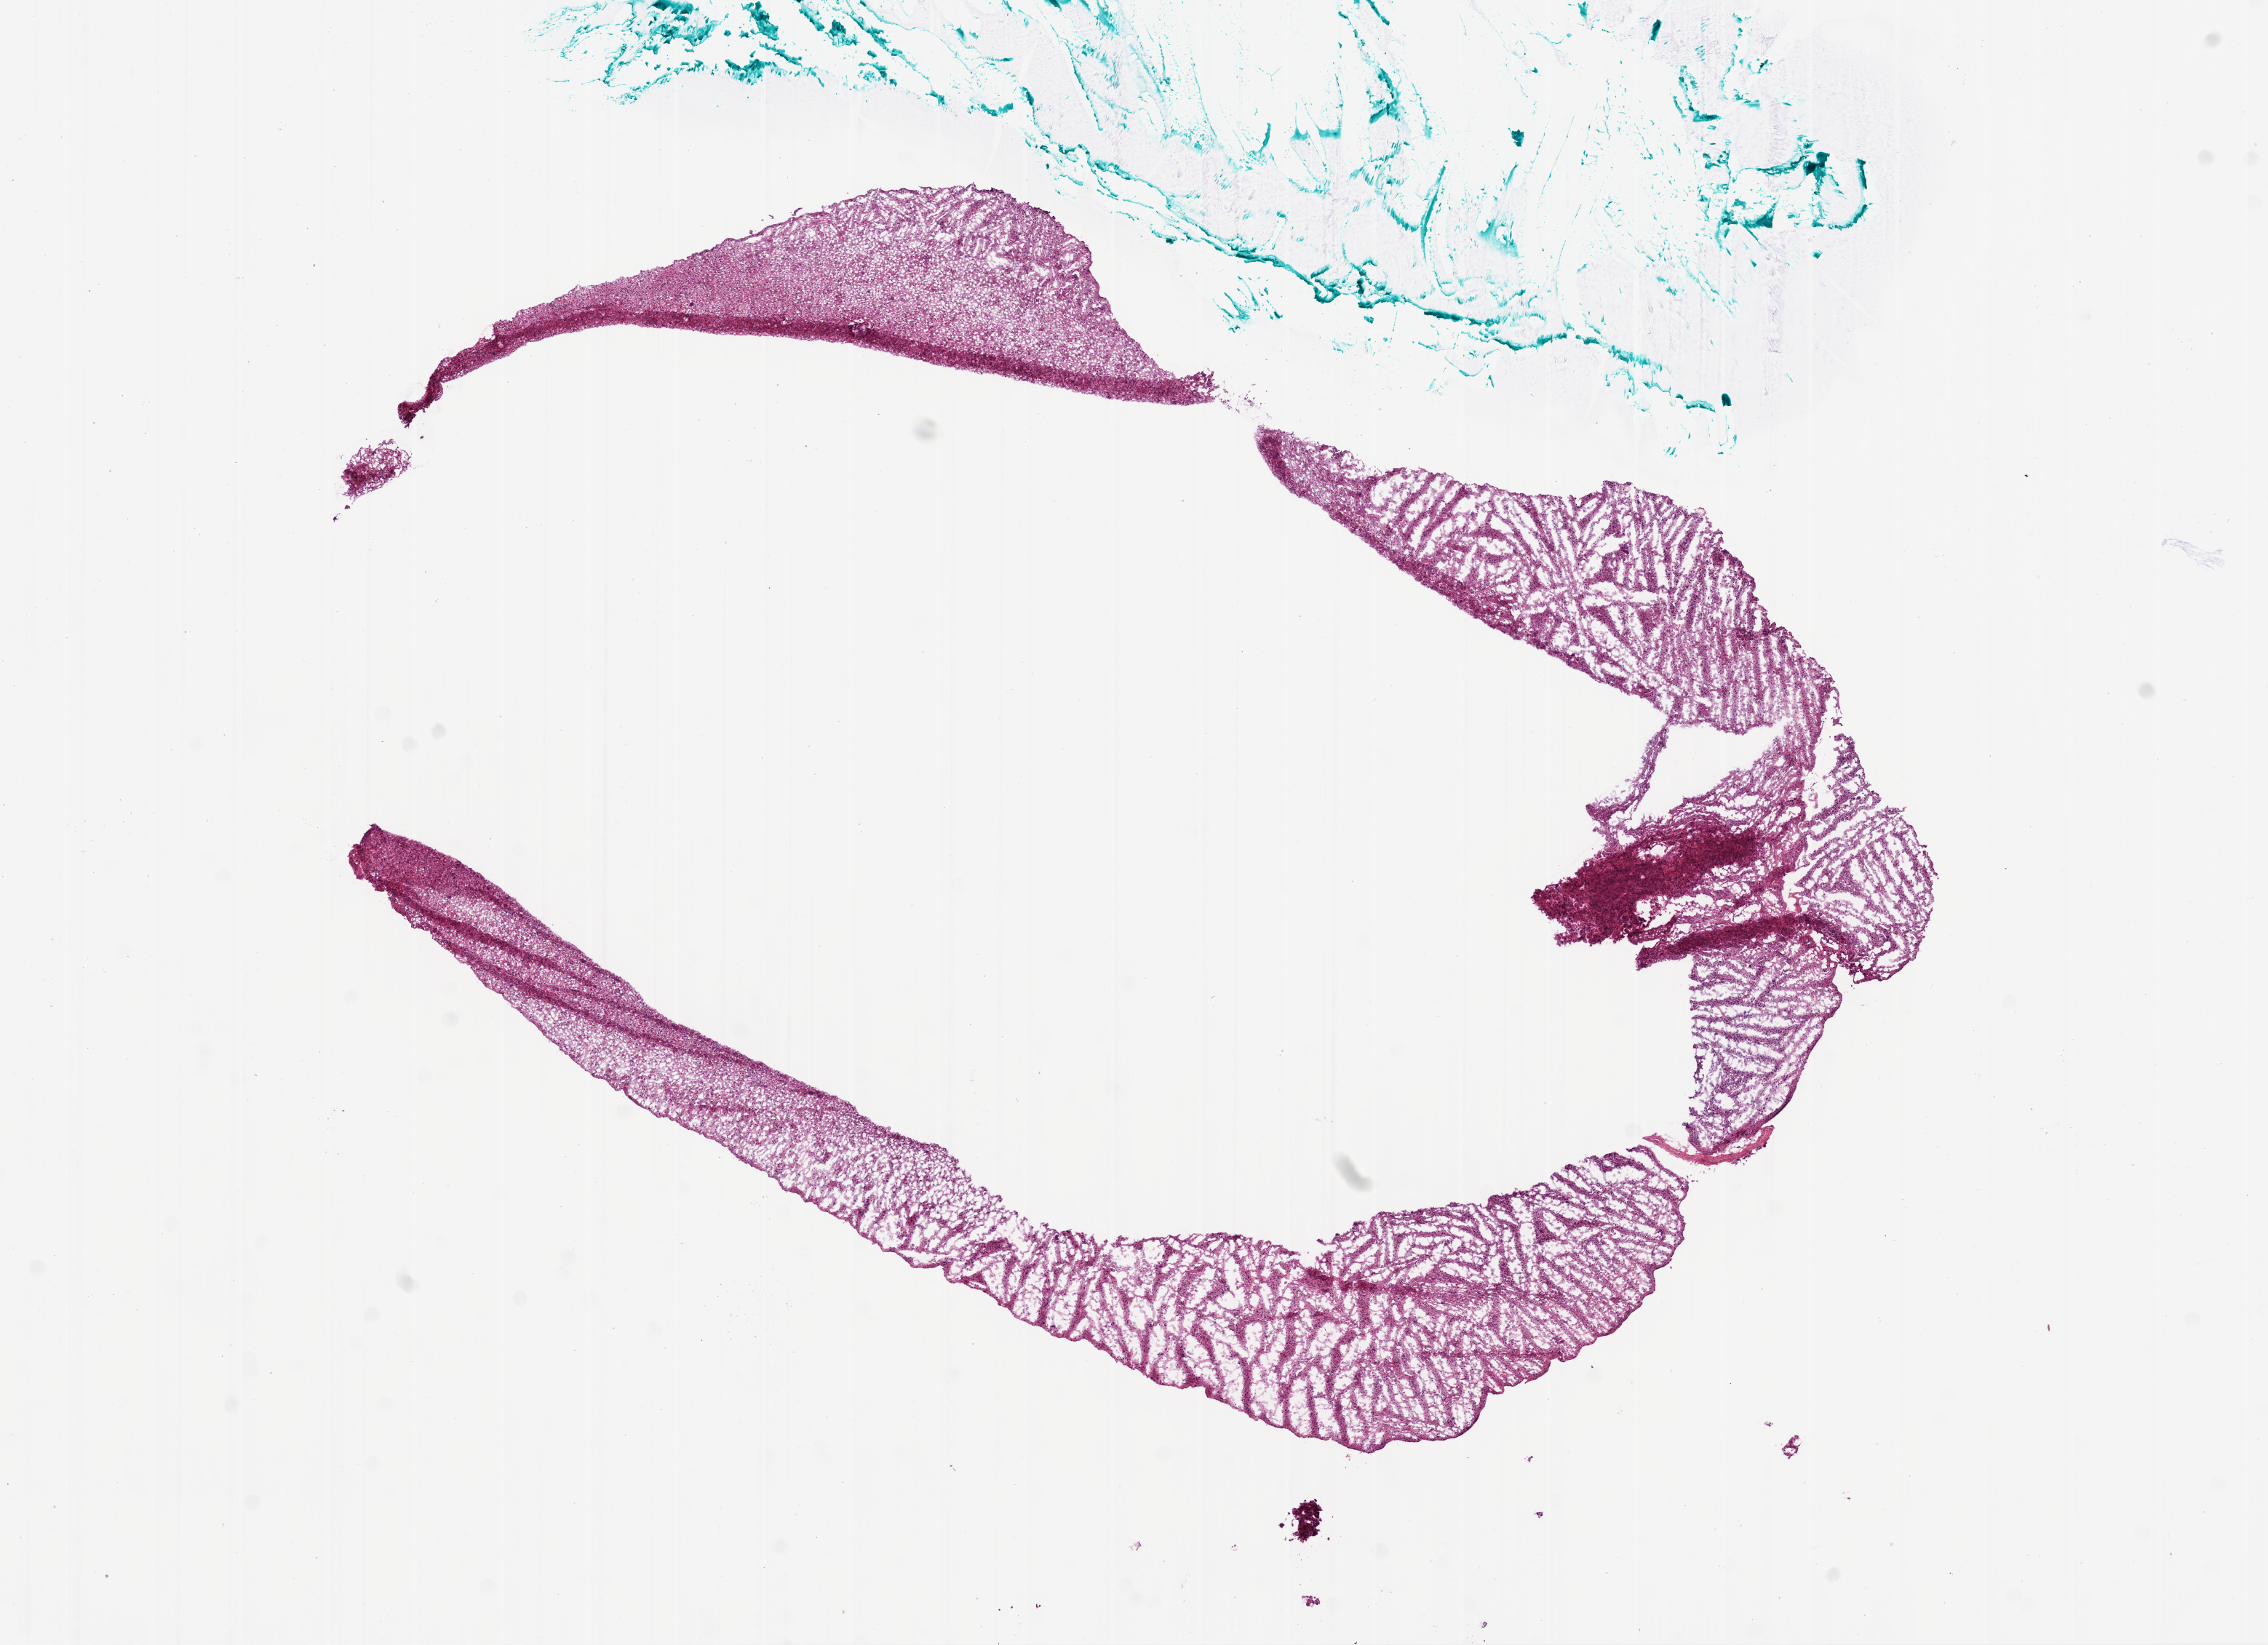
Hematoxylin and eosin (H&E) stained whole-slide image — whole scanned area (about 12.6 x 9.1 mm, acquisition: 20x scan) shown as a low-resolution overview; frozen section from the bottom of the tissue portion; primary tumour sample from the brain. Patient: male, age at initial diagnosis 63 years. Pathologist review of this section (percent, as recorded): tumour cells 100%, tumour nuclei 100%, normal cells 0%, stromal cells 0%, necrosis 0%.
Histologic diagnosis: Glioblastoma.